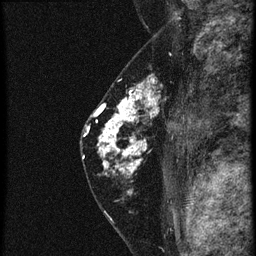
Breast MRI (dynamic contrast-enhanced), one sagittal slice; position 38 of 60 along the scan axis; 4 images stored at this slice position (order not interpretable as contrast timing); 1.5 T; TE 4.2 ms, TR 20.4 ms; 256 × 256 image matrix. Patient: female, 46 years. From the clinical record (not read from this slice): setting: breast cancer imaged before/during neoadjuvant chemotherapy; receptor status: triple-negative.
Structures marked on this image (semi-automatically segmented with operator editing):
- analysis volume of interest (the breast-tissue region the enhancement analysis was run in; not a lesion): bounding box <88,82,181,185> (left, top, right, bottom; pixels)
- tumour enhancement mask (voxels above the 90 % enhancement threshold inside the analysis volume of interest): <88,82,157,175>